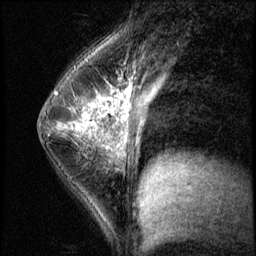
Breast MRI (dynamic contrast-enhanced), one sagittal slice; slice 35 of 56 in the series (ordered by position); 3 images stored at this slice position (order not interpretable as contrast timing); 1.5 T; TE 4.2 ms, TR 8.7 ms; 2.5 mm slice thickness; 256 × 256 image matrix, field of view 180 × 180 mm. Female patient, age 35 years. From the clinical record (not read from this slice): setting: breast cancer imaged before/during neoadjuvant chemotherapy; receptor status: HER2-positive.
Annotated regions visible in this slice (semi-automatic segmentation, software-assisted and operator-edited):
- analysis volume of interest (the breast-tissue region the enhancement analysis was run in; not a lesion): box from (x=58, y=84) to (x=138, y=186) px
- tumour enhancement mask (voxels above the 140 % enhancement threshold inside the analysis volume of interest): (x=58, y=92)–(x=103, y=139)